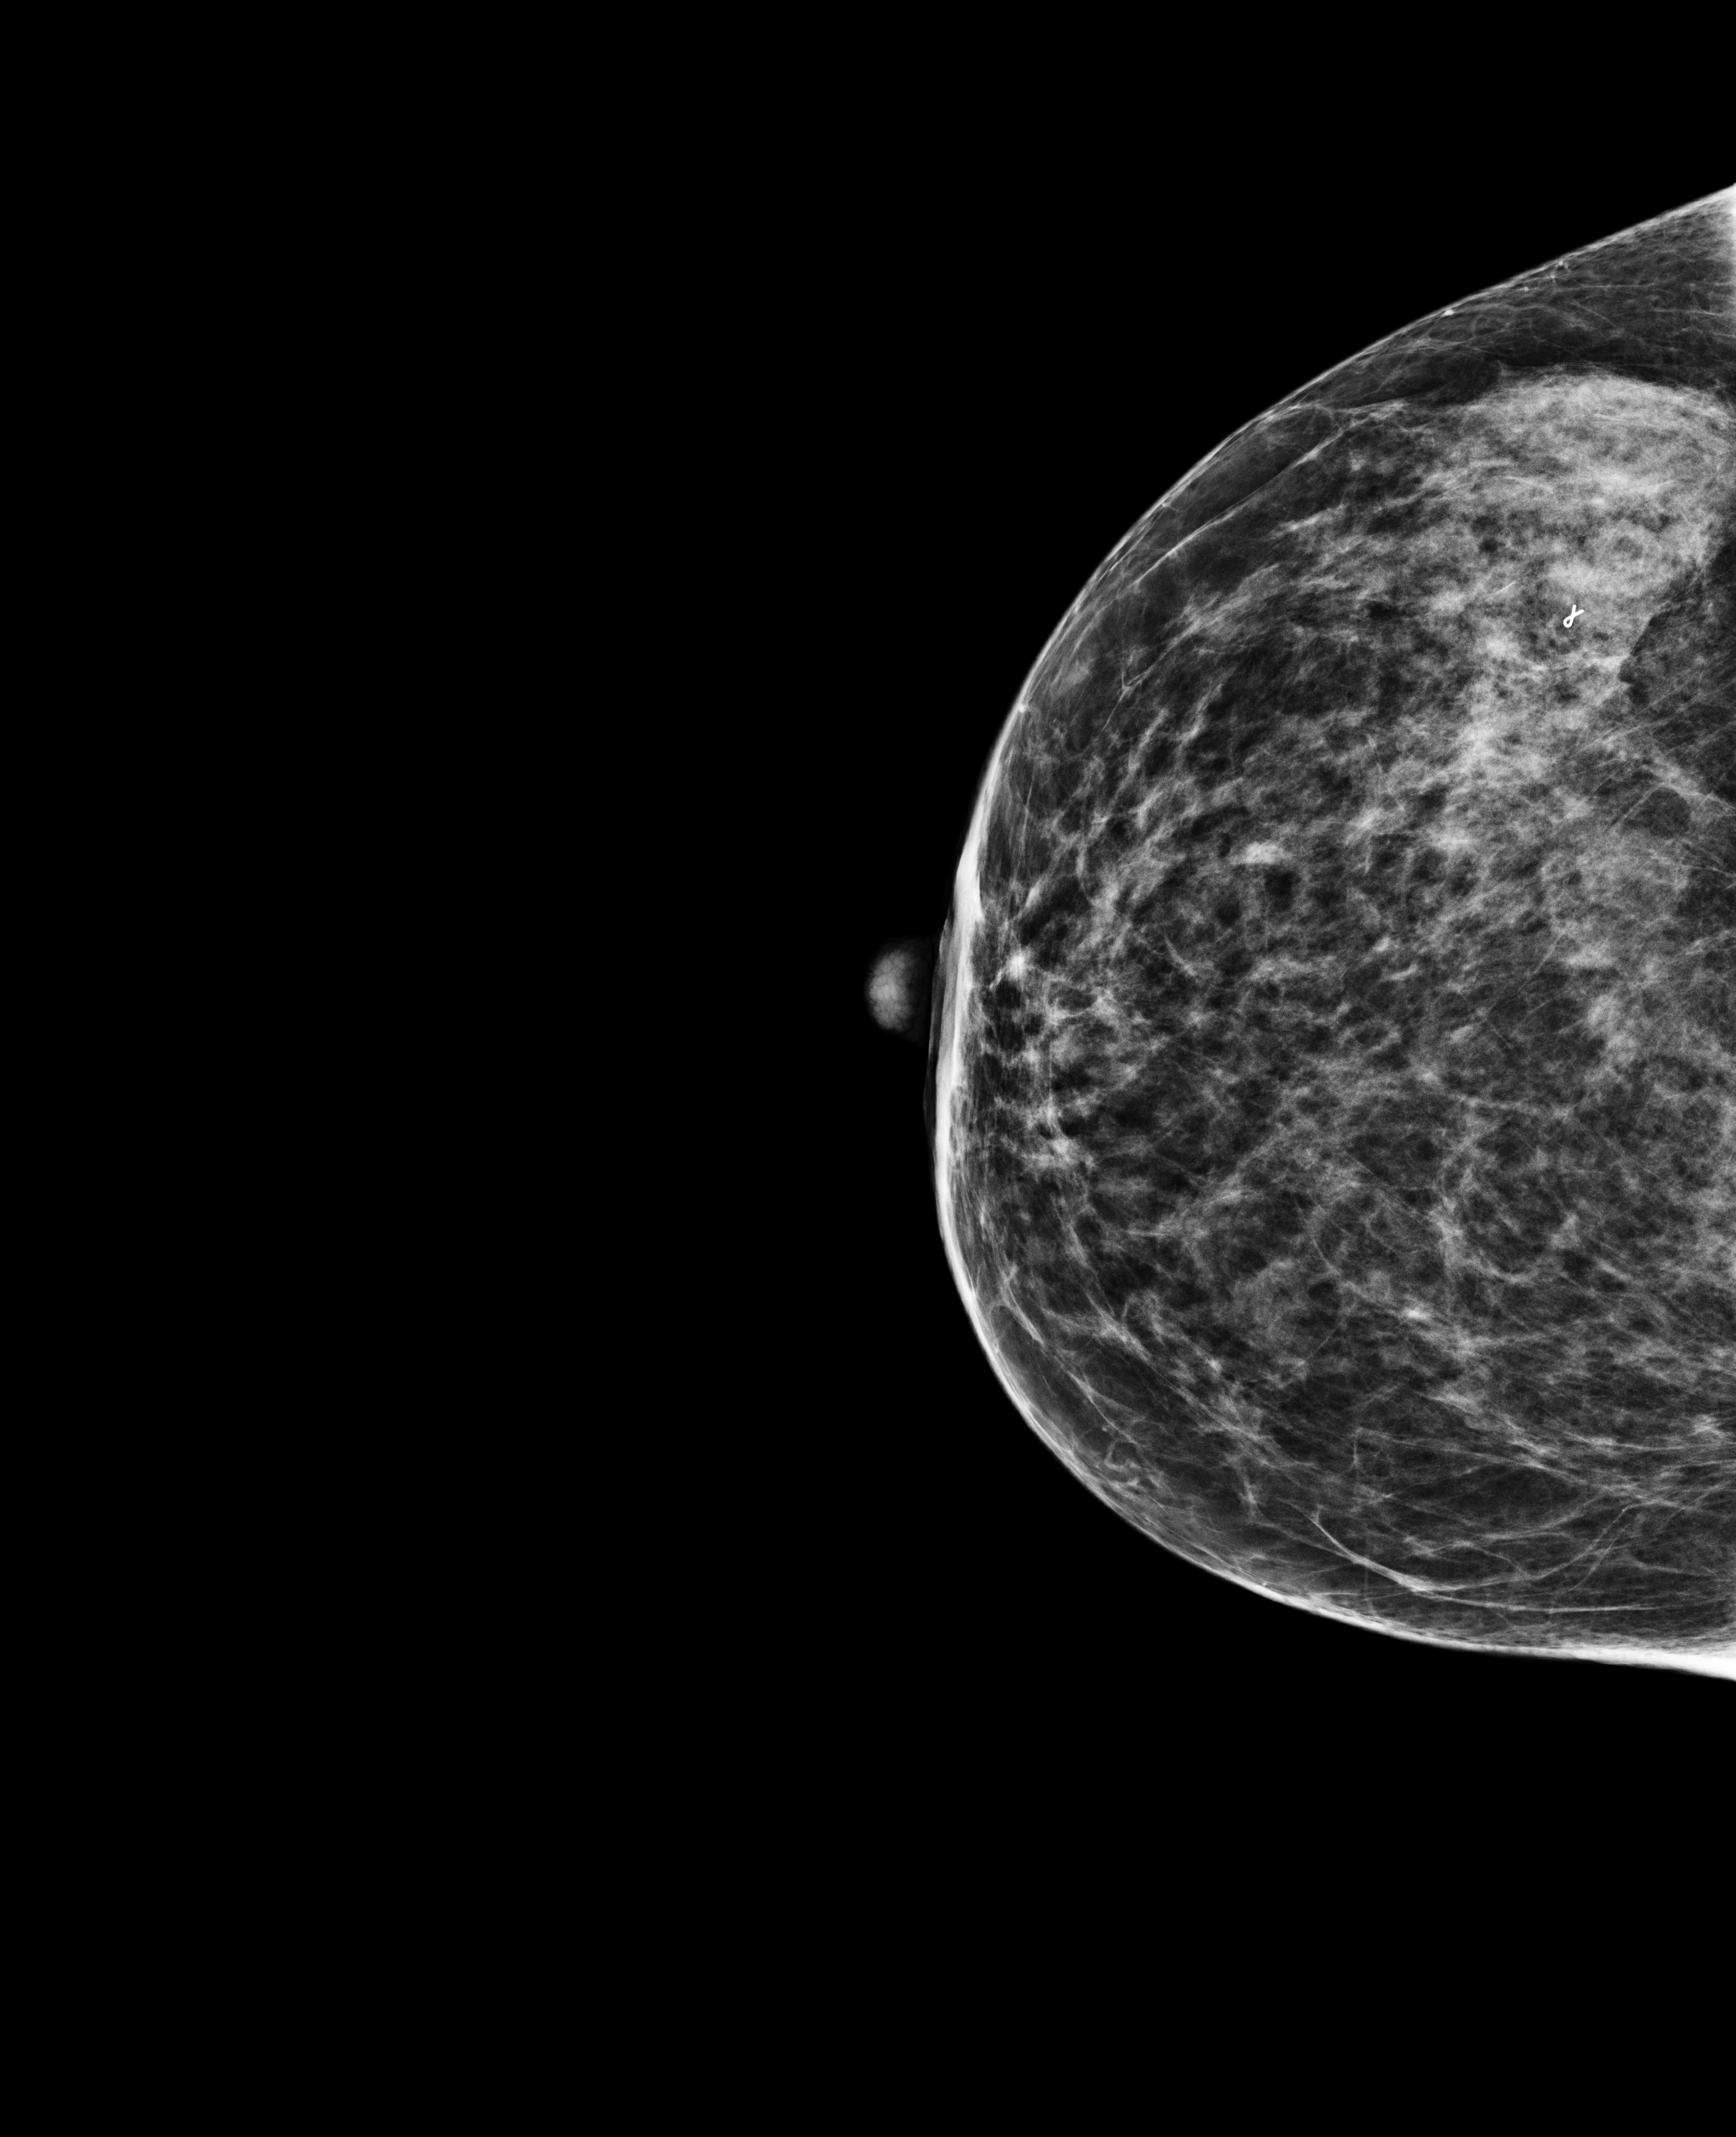
Screening examination, compressed breast thickness 49 mm, system: Selenia Dimensions.
Image type: full-field digital mammogram. Breast: right. Projection: cranio-caudal projection.